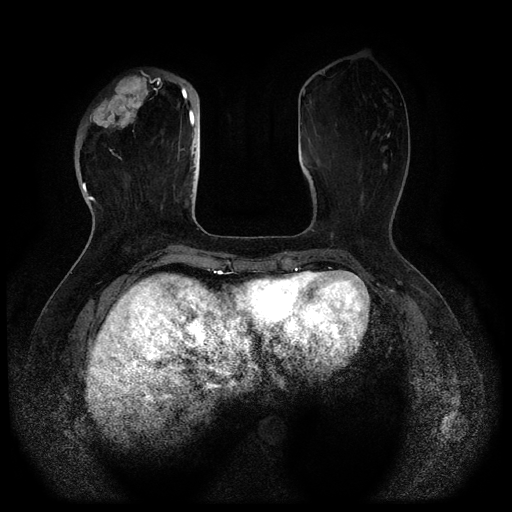
Breast MRI (dynamic contrast-enhanced, multi-phase), one axial slice. Dynamic contrast-enhanced series, time point 2 of 5 at this slice position (early post-contrast). 1.5 T. TE 2.6 ms, TR 5.3 ms. 512 × 512 image matrix. Female patient, age 51 years.
Structures marked on this image (semi-automatically segmented with operator editing):
- breast lesion (labelled 'tumour' in the annotation; benign lesions carry a separate 'benign' label): bounding box (x1, y1, x2, y2) in pixels: (90, 73, 149, 130)